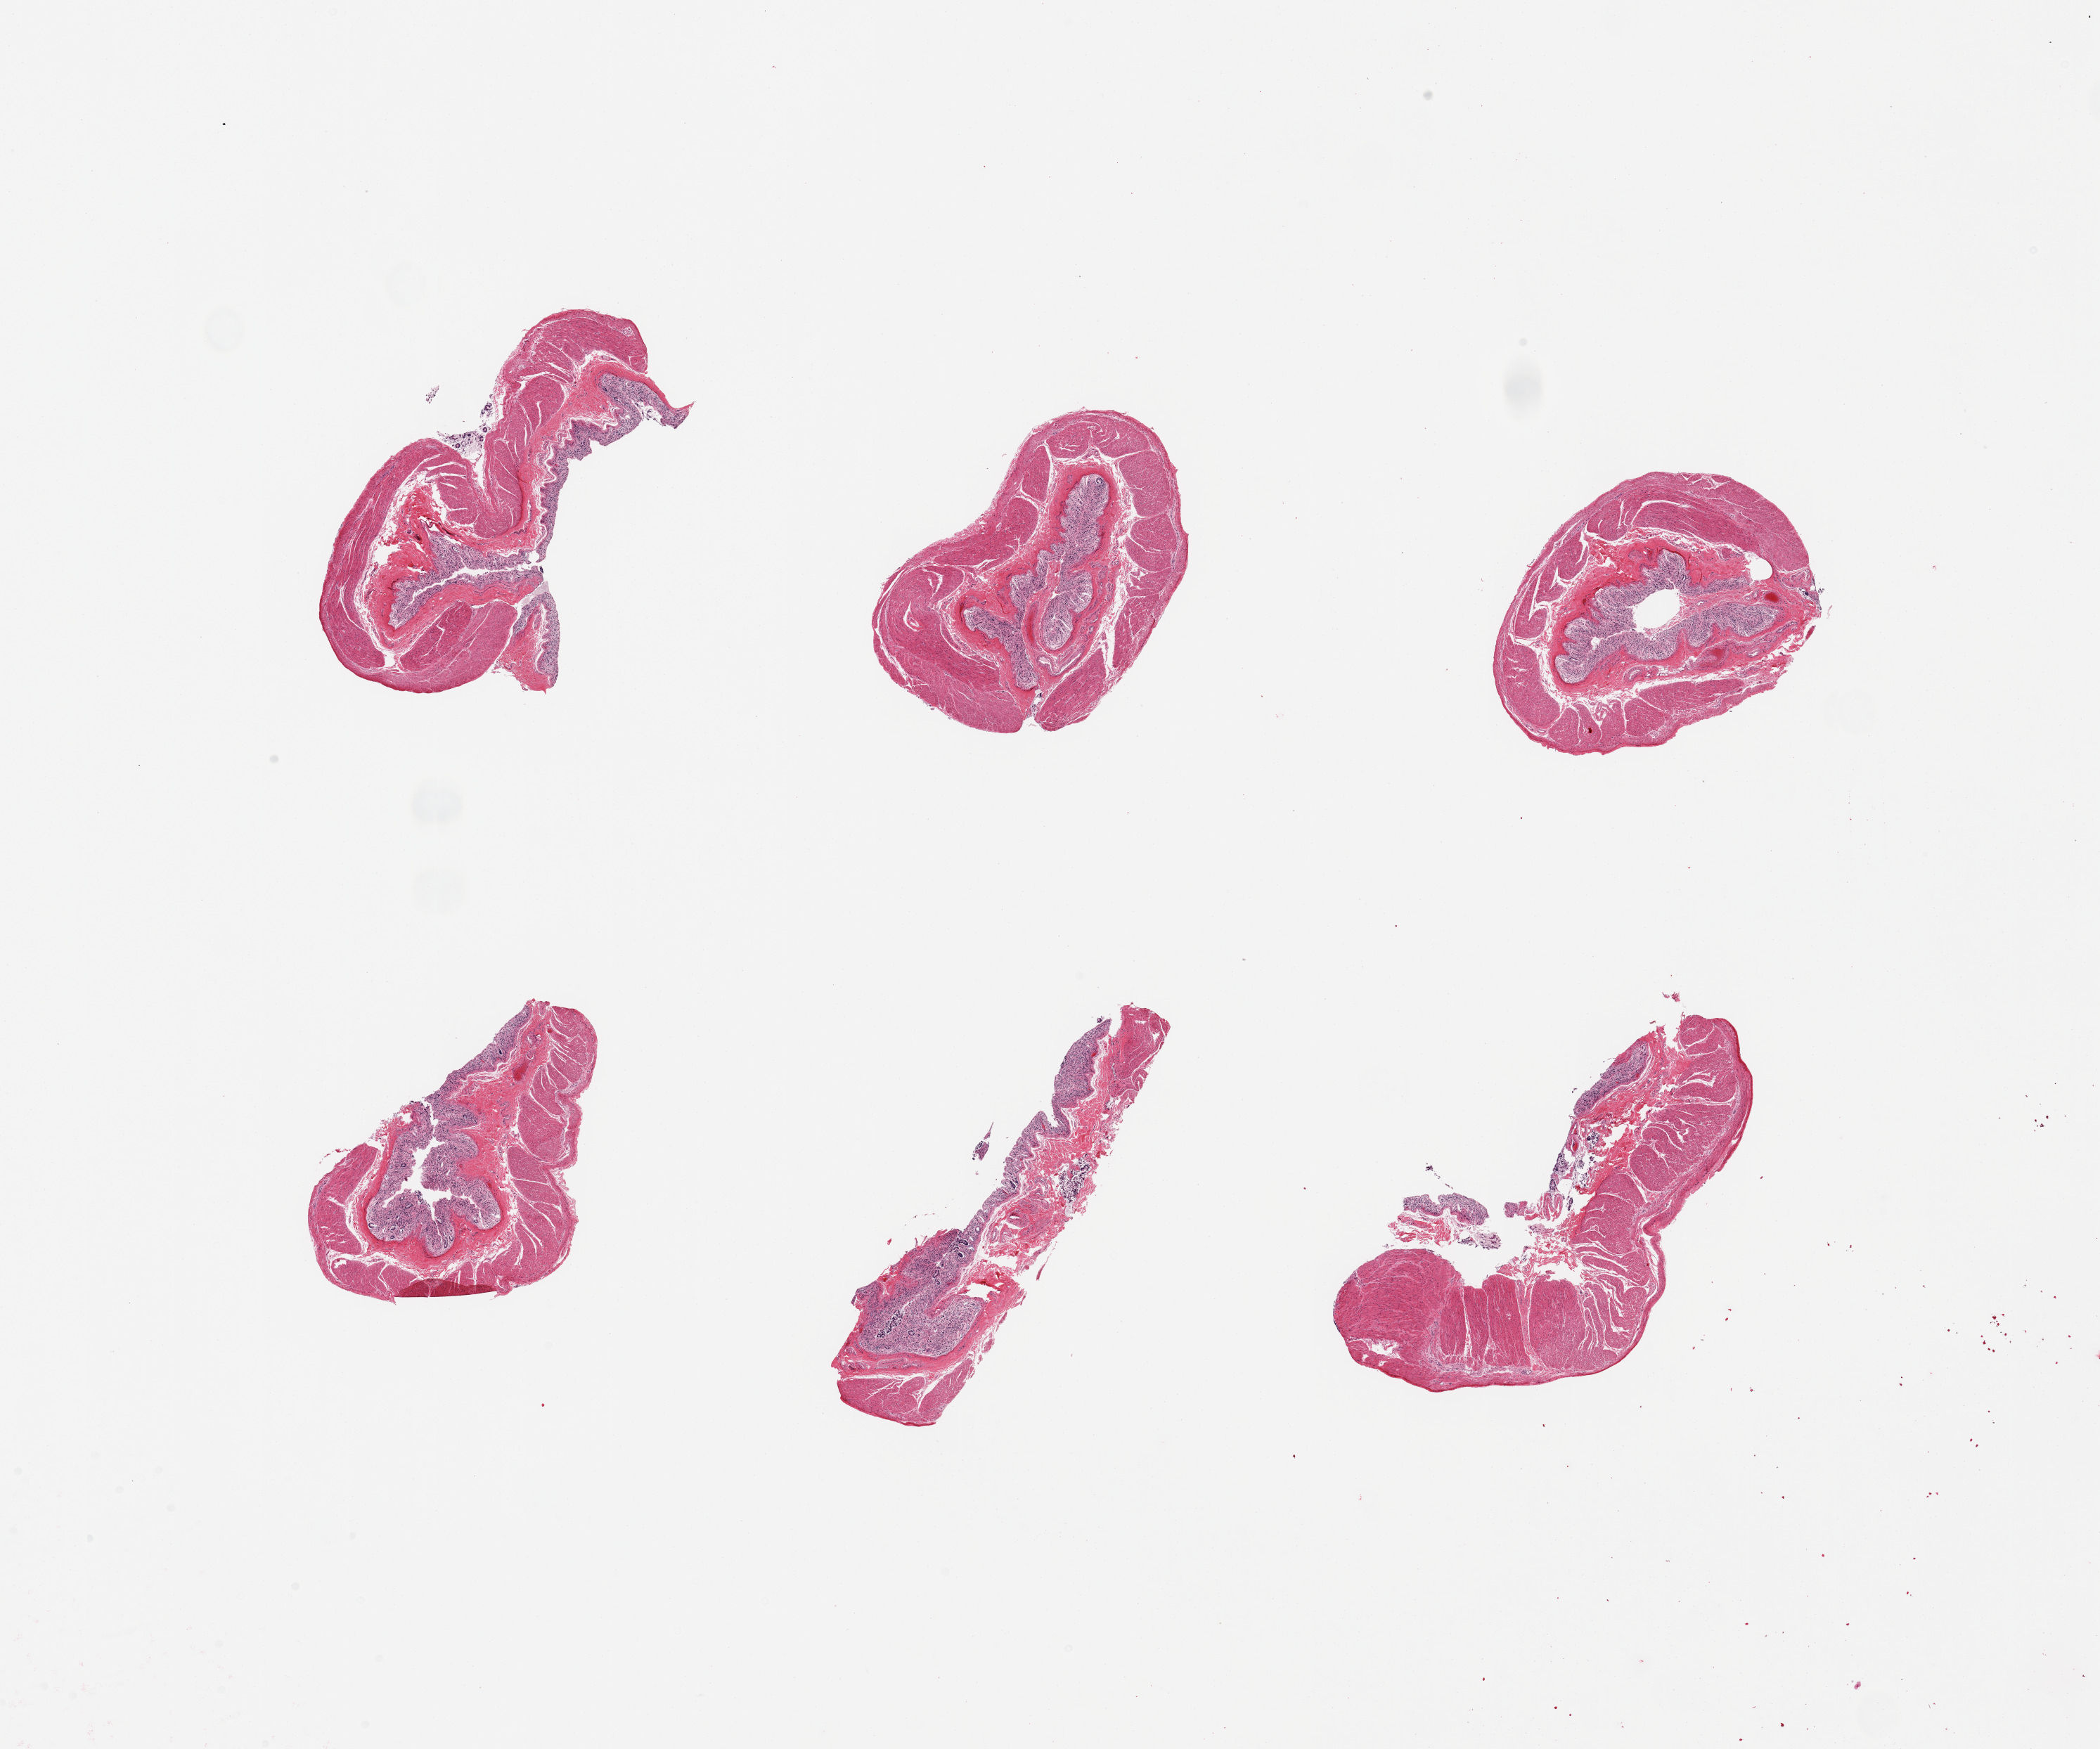
Whole-slide image, hematoxylin and eosin (H&E) stain, low-resolution overview of the scanned area, about 23.6 x 19.7 mm, PAXgene-fixed, paraffin-embedded tissue, section of transverse colon (target tissue), tissue donor sample. Donor sex: male.
Pathologist's review note for this sample: 6 pieces; mucosa autolyzed, muscle intact.